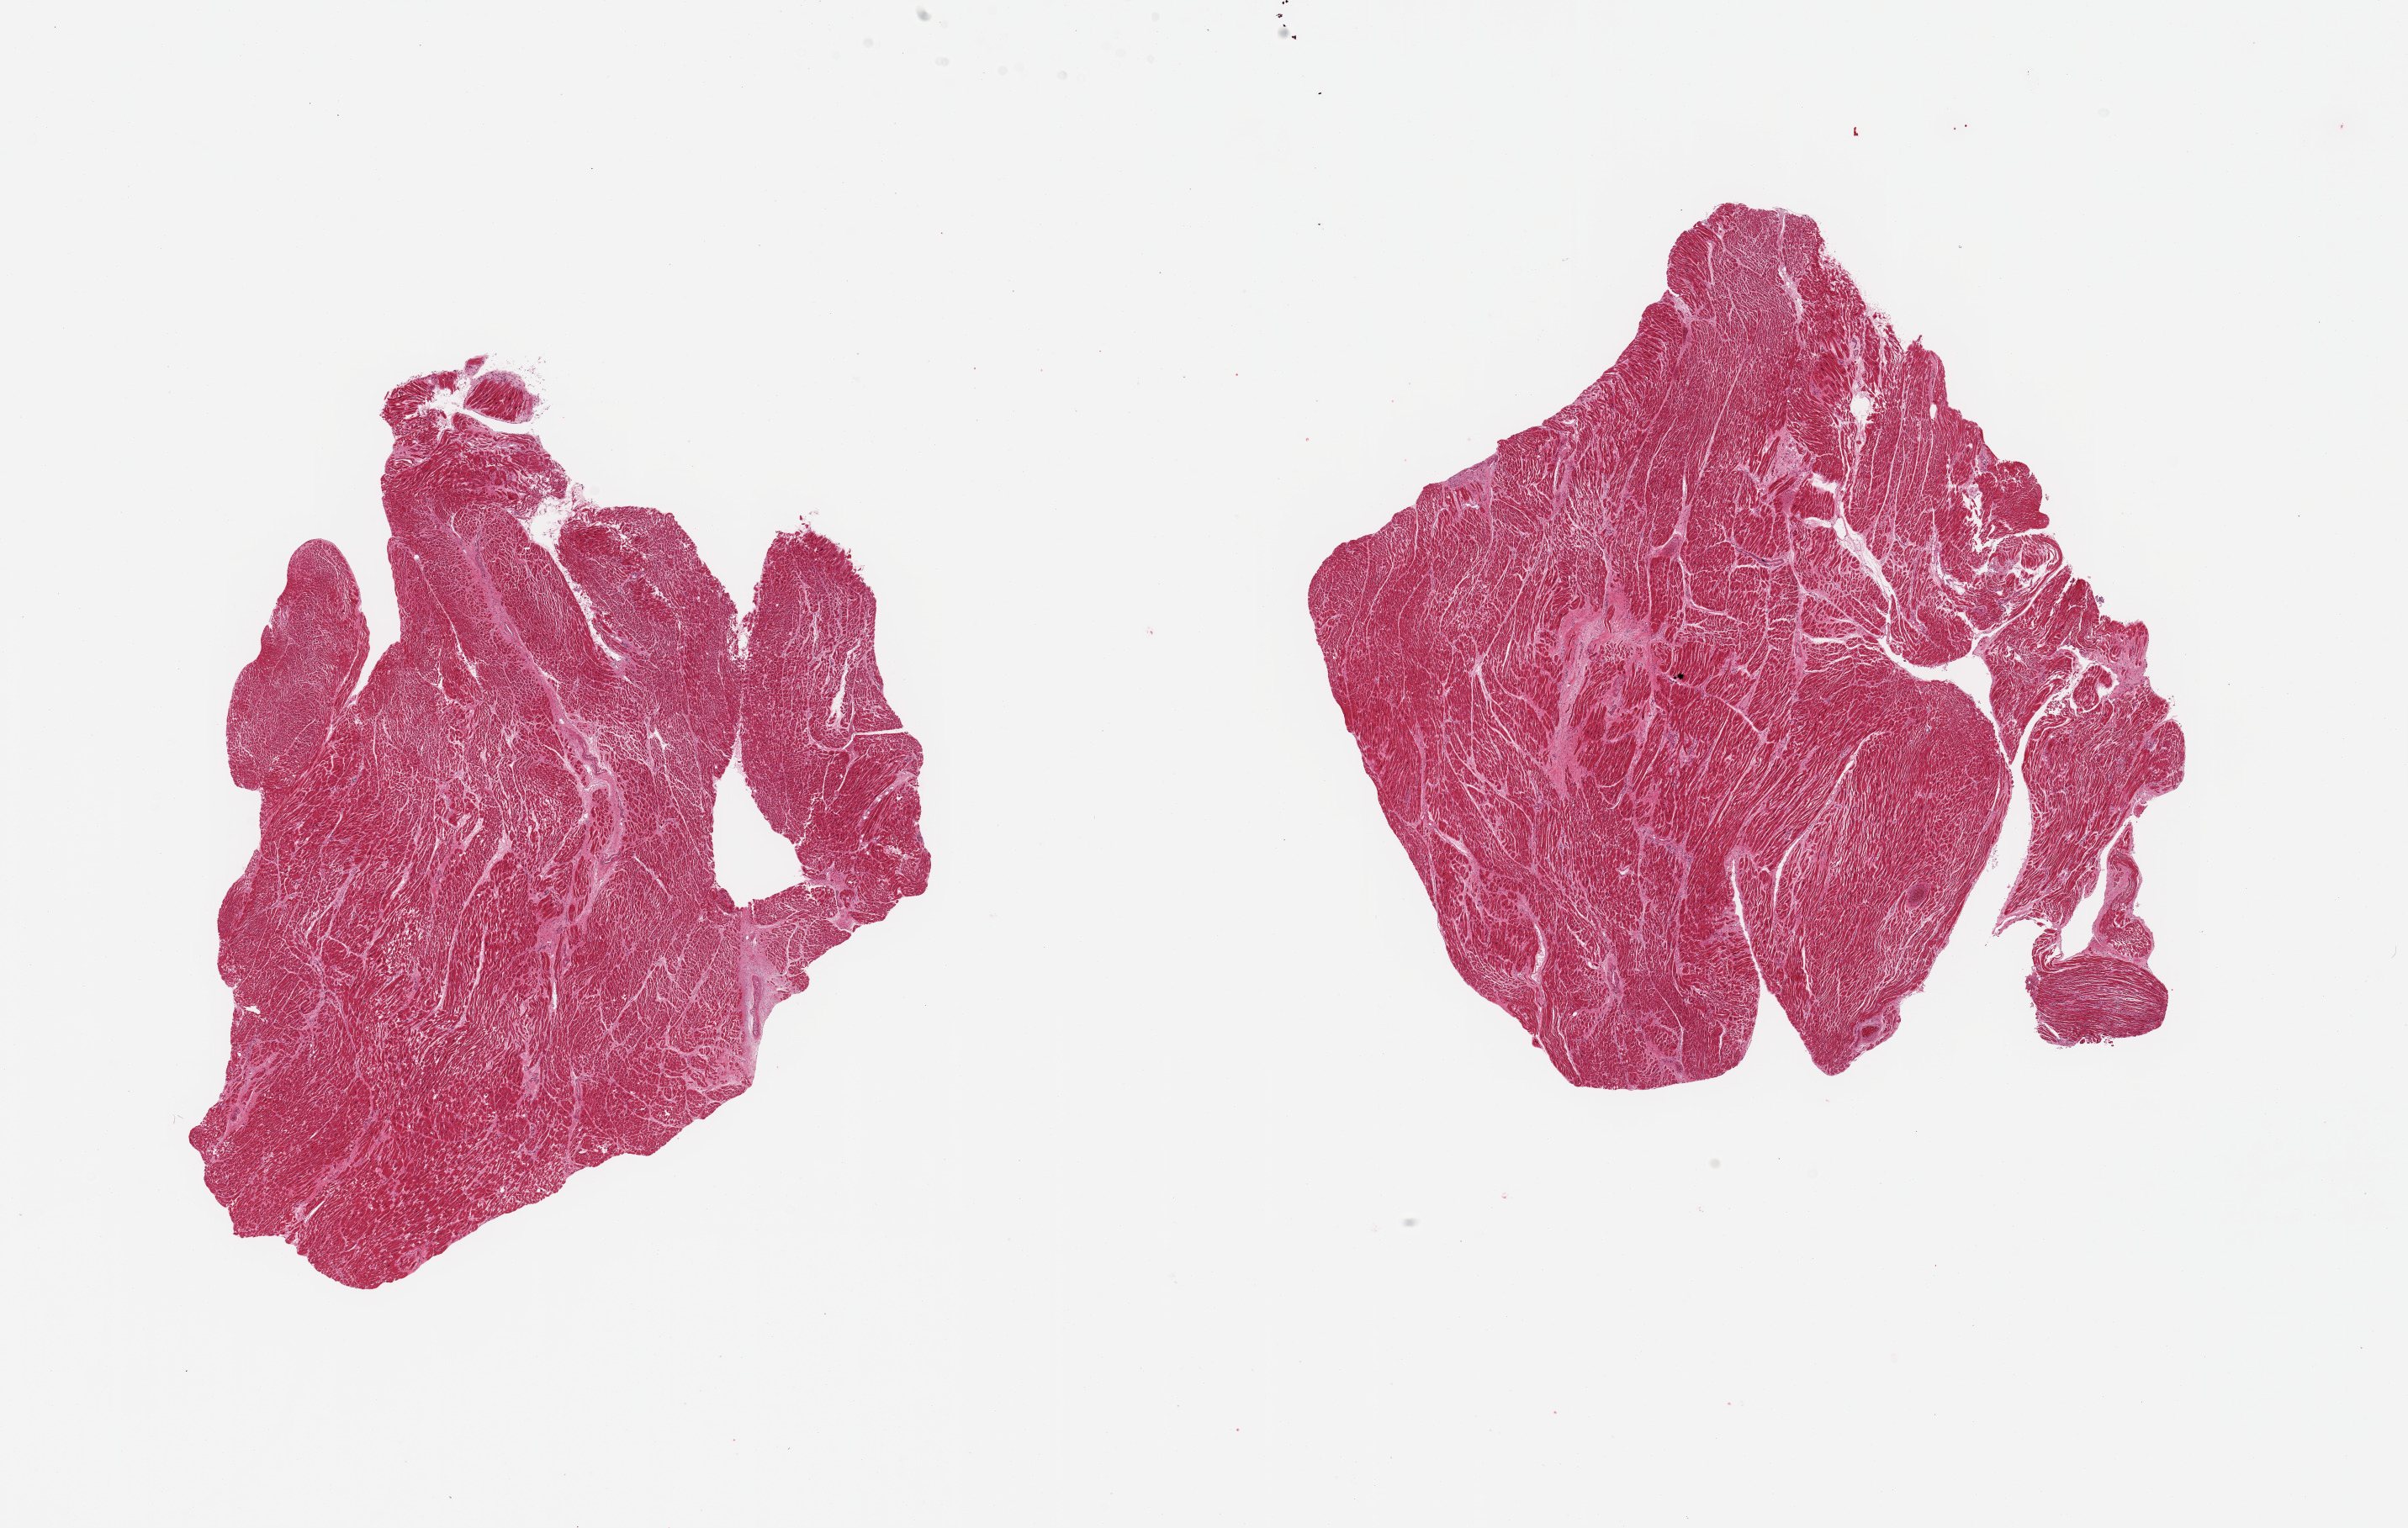
Haematoxylin and eosin whole-slide image, brightfield — shown as a low-resolution overview of the whole scanned area (about 22.6 x 14.4 mm, from a 20x scan), PAXgene-fixed paraffin-embedded (PFPE) section, sampled site (target tissue): heart, donor tissue sample.
Pathologist's review note for this sample: 2 pieces, moderate chronic ischemia/interstial fibrosis, microinfarcts up to ~2x1mm noted.